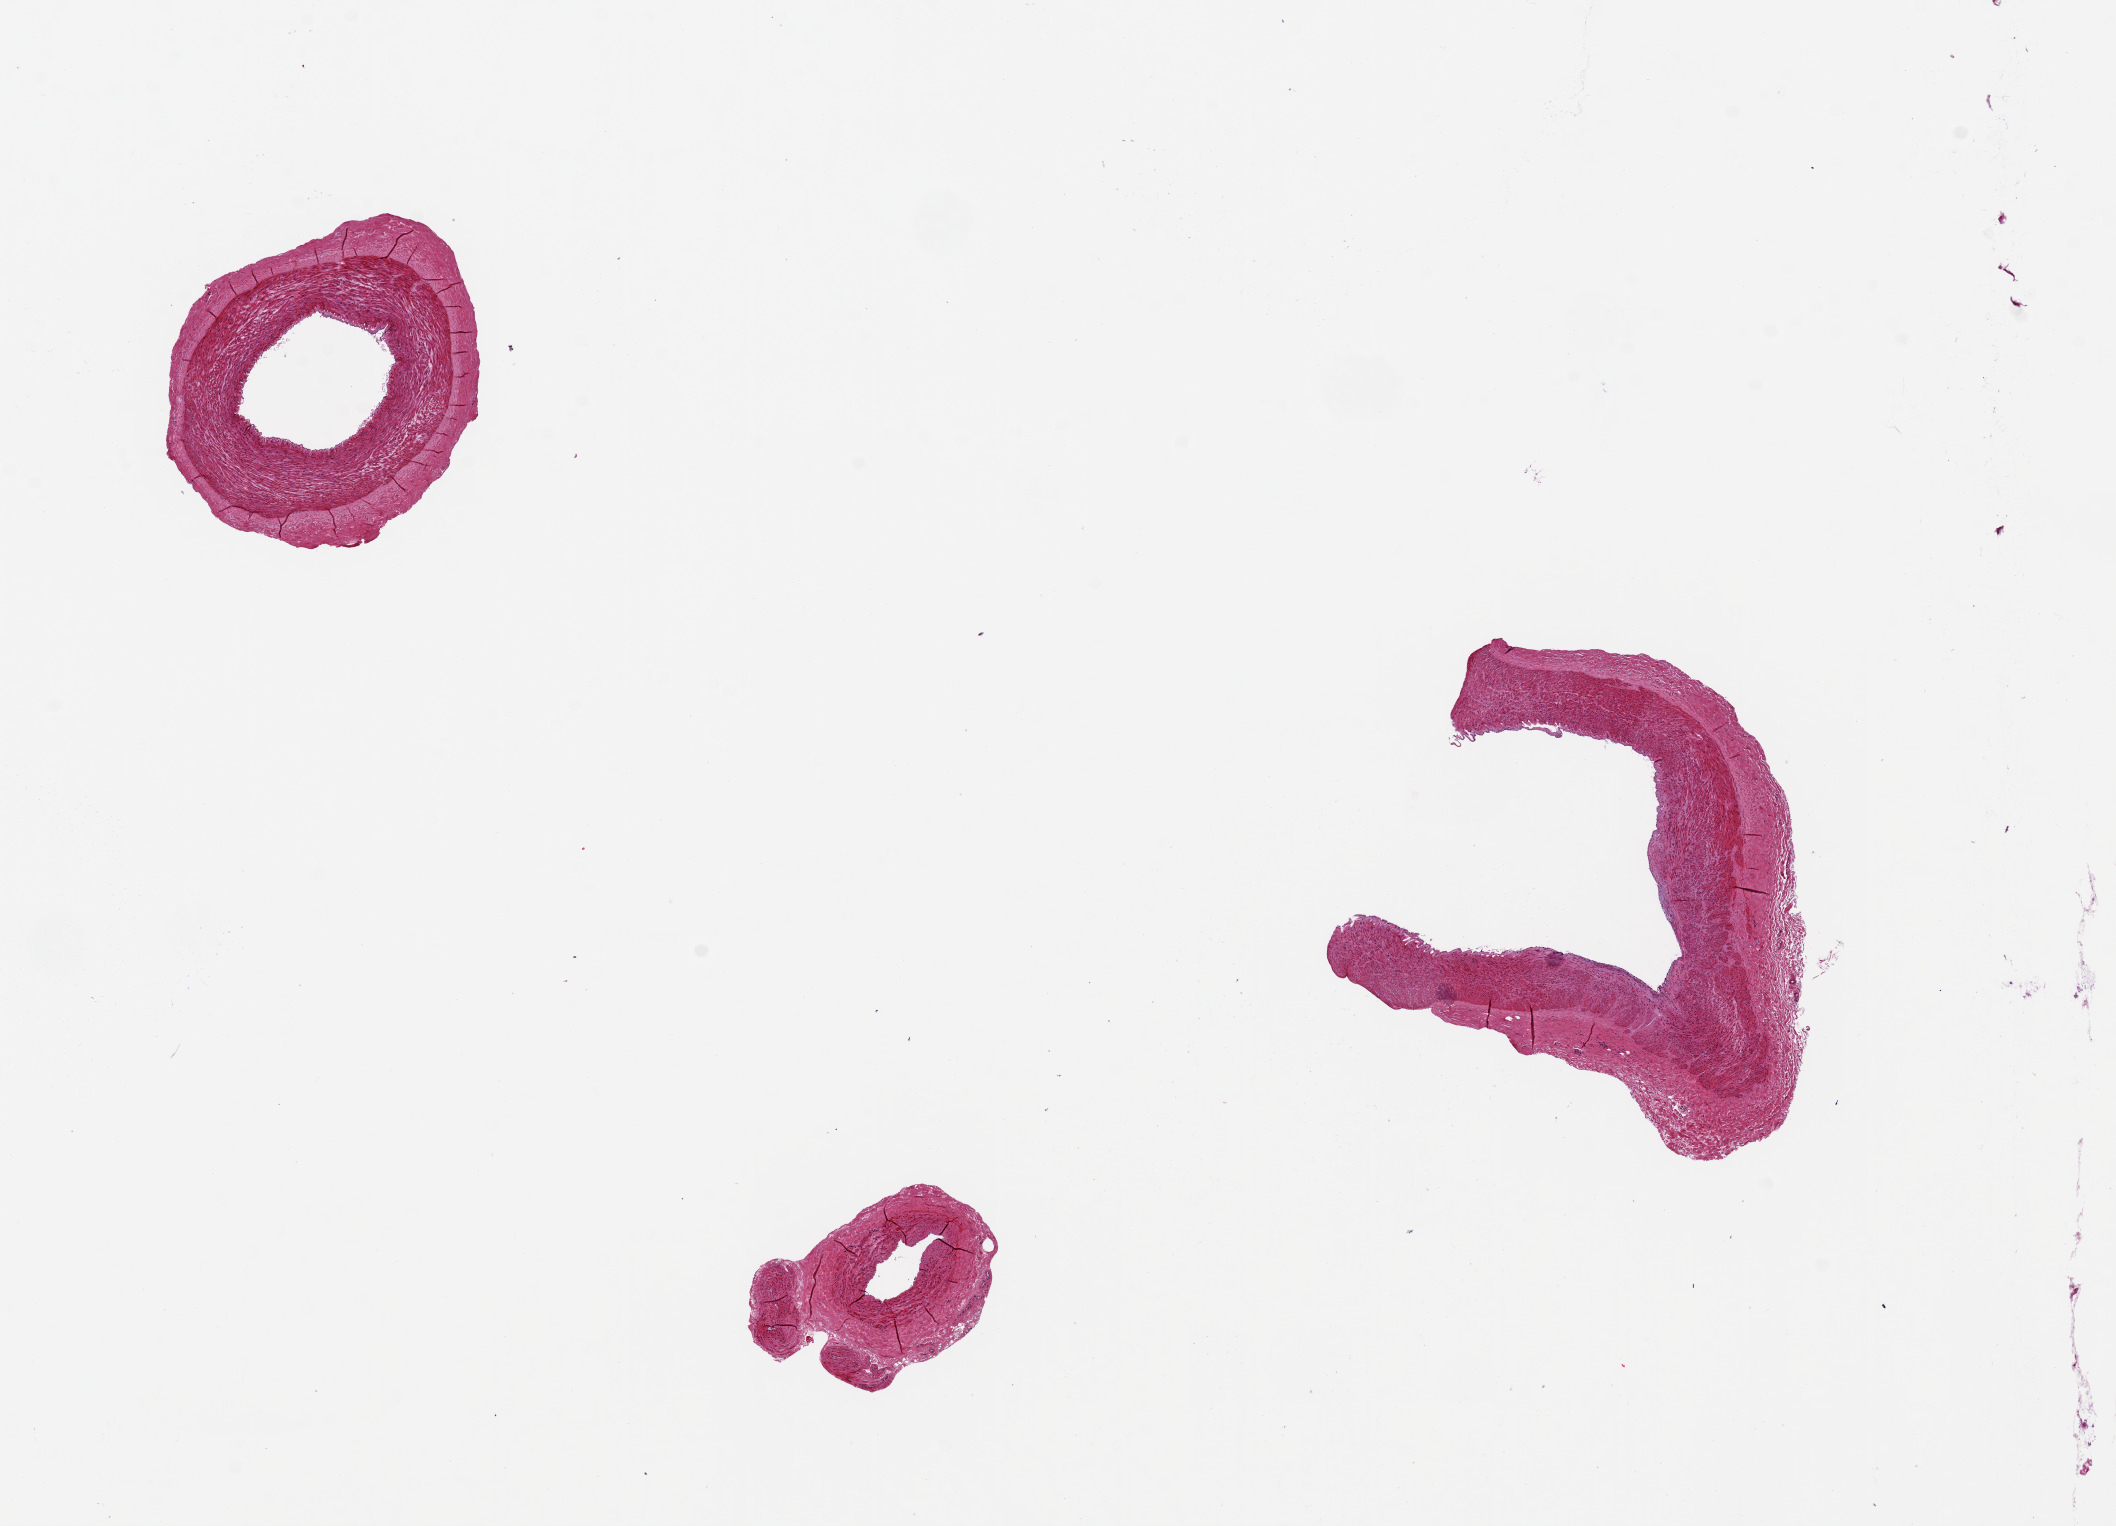
Haematoxylin and eosin whole-slide image — whole scanned area (about 16.7 x 12.1 mm, acquisition: 20x scan) shown as a low-resolution overview. PAXgene-fixed paraffin-embedded (PFPE) section. Section of tibial artery (target tissue). Tissue donor sample. Donor sex: female.
Pathologist's review note for this sample: 3 pieces, up to 4x3mm; no extraneous adipose.